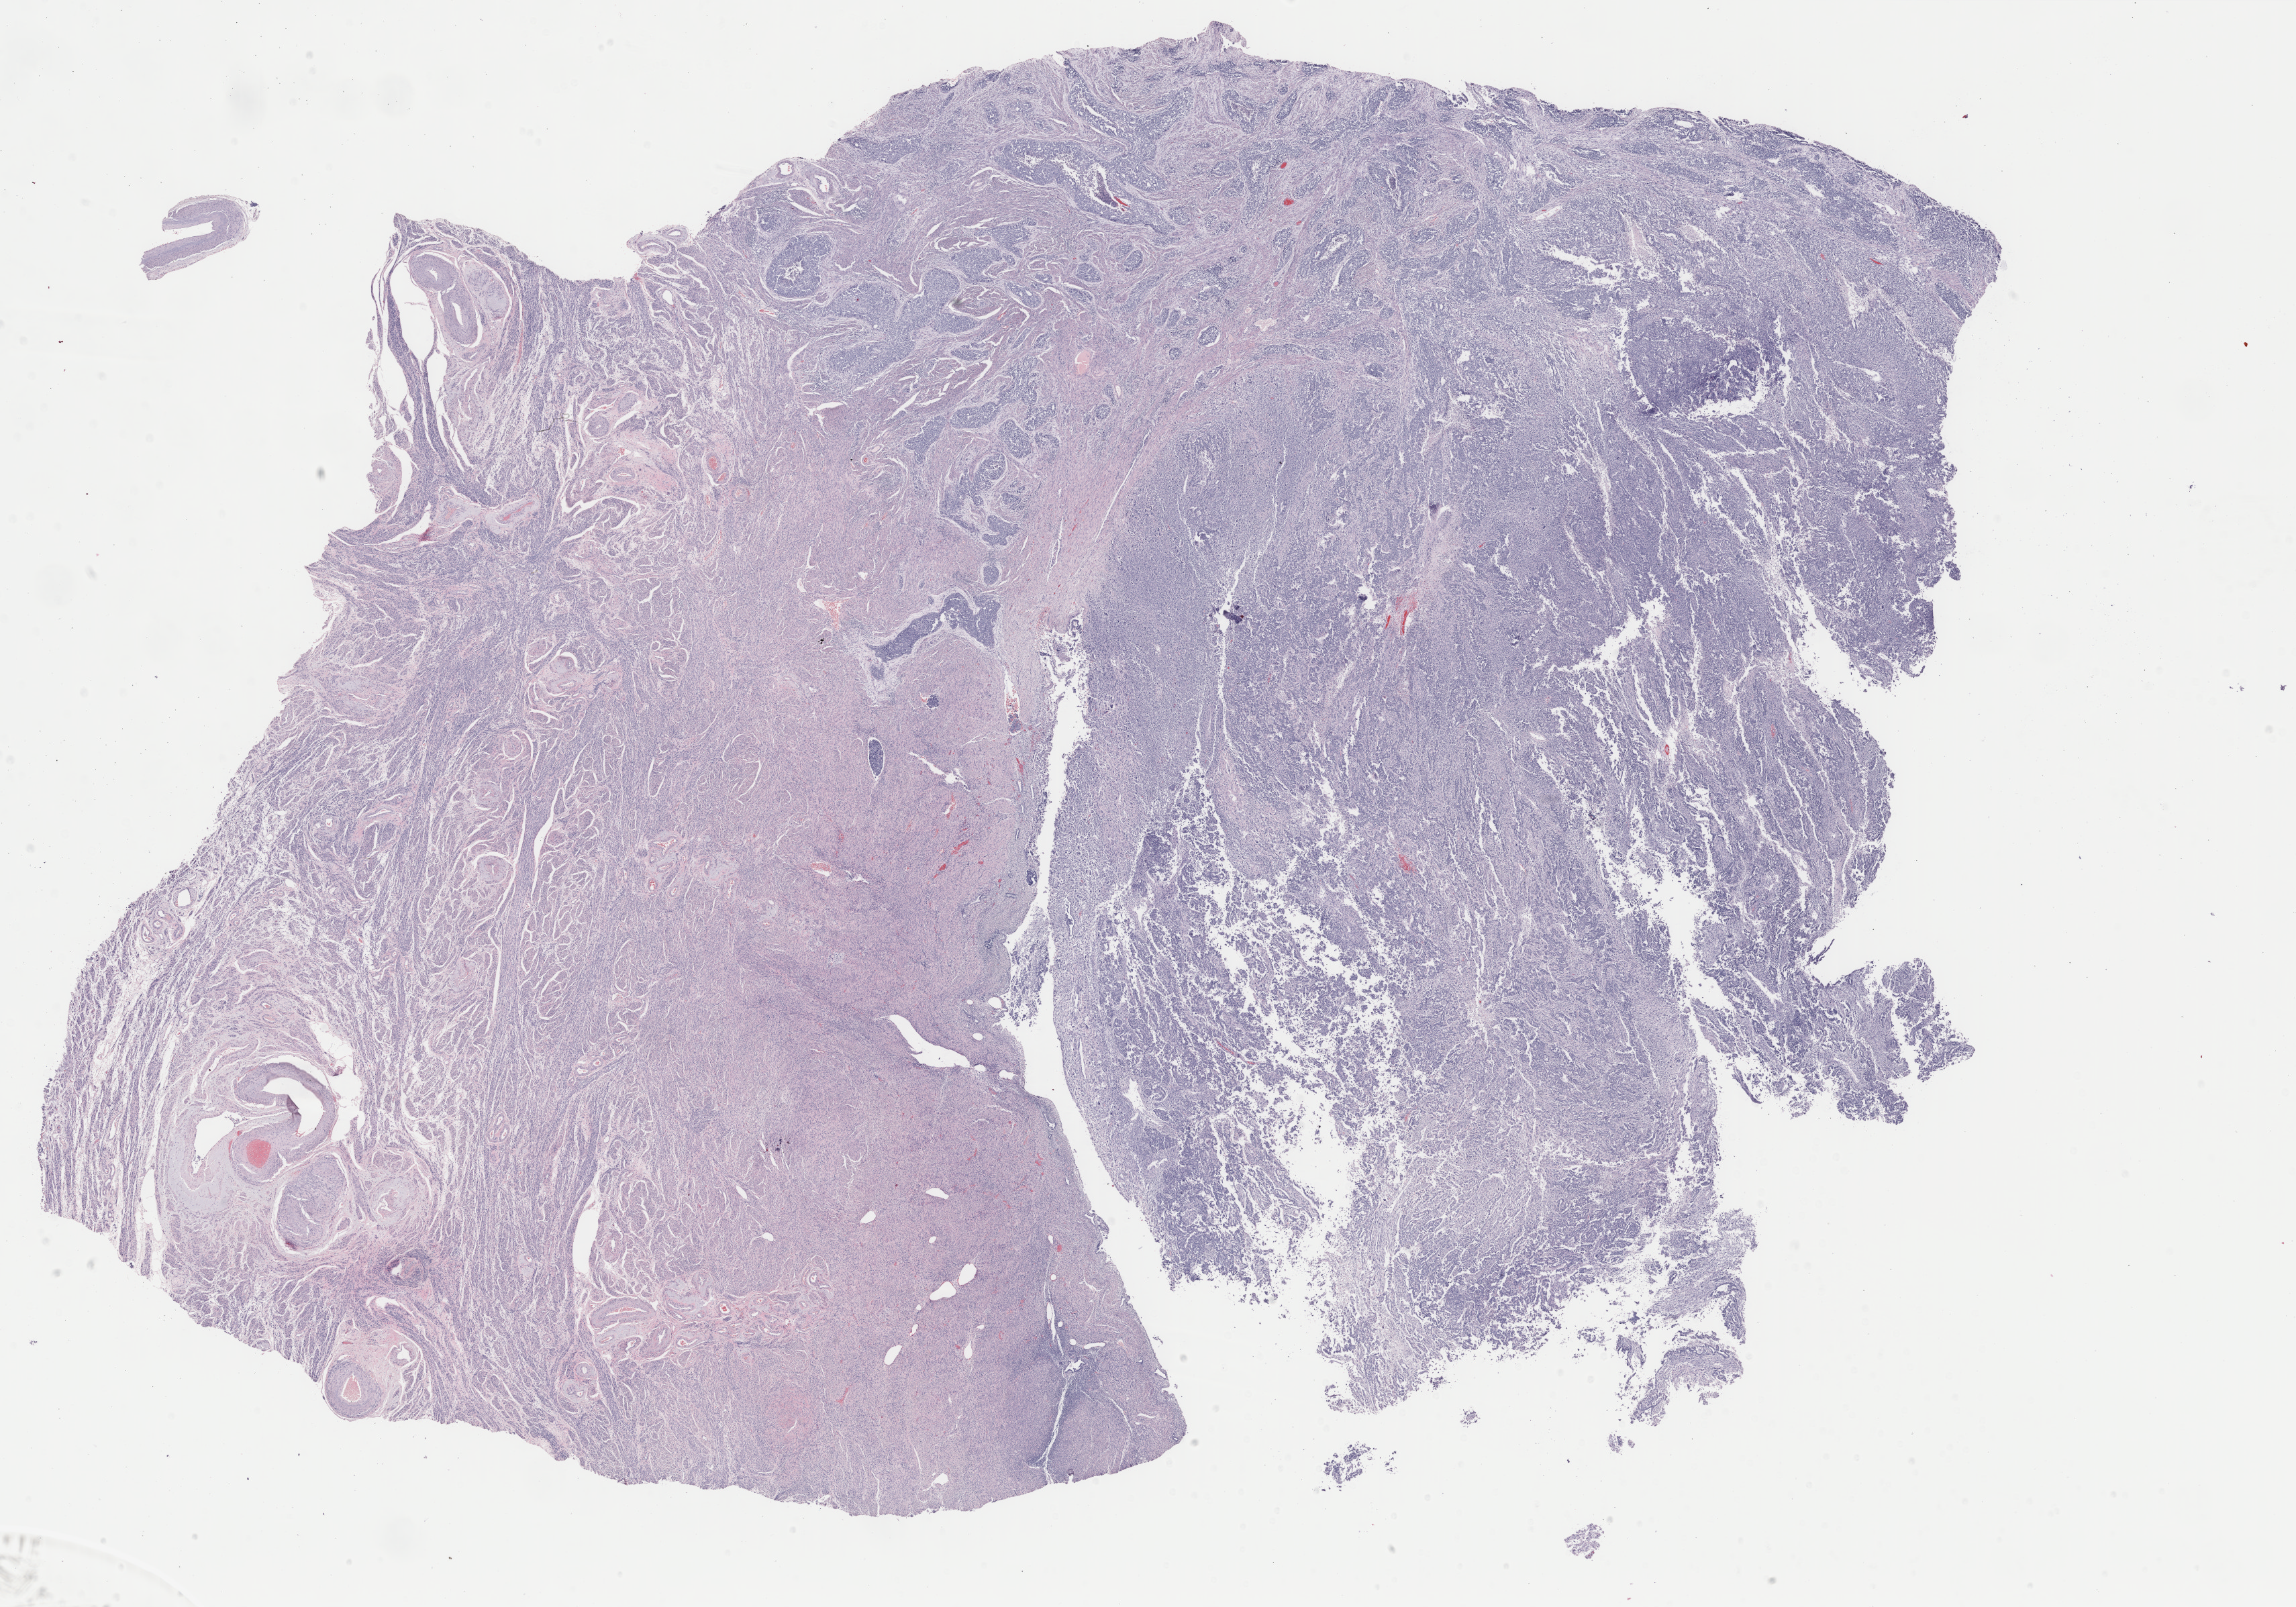
Whole-slide histology image, Hematoxylin and eosin (H&E) stained, shown as a low-resolution overview of the whole scanned area (about 27.2 x 19.0 mm), formalin-fixed paraffin-embedded (FFPE) diagnostic section, primary tumour sample from the uterus. Female patient; age at initial diagnosis 65 years.
• FIGO stage: IB
• pathologic diagnosis: Mullerian mixed tumor
• lymph nodes positive (case pathology): 0 of 12 examined